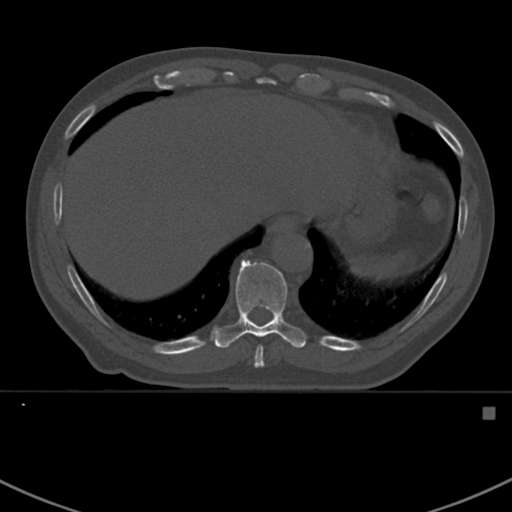
CT including the spine, one axial slice; slice 368 of 412 in the series (ordered by position); reconstruction kernel Br40s; 120 kVp; bone window (W 1800 / L 400 HU); 512 × 512 image matrix. Patient: male, 59 years. From the clinical record (not read from this slice): primary cancer: prostate.
Outlined on this slice (semi-automatic segmentation, software-assisted and operator-edited):
- T10 vertebra: bounding box [x1, y1, x2, y2] px = [214, 258, 306, 368]
- T9 vertebra: [255, 346, 263, 366]